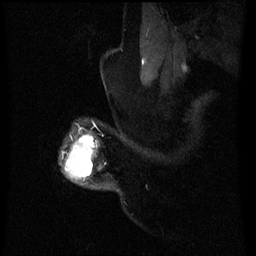
Breast MRI (dynamic contrast-enhanced), one sagittal slice; slice 55 of 60 in the series (ordered by position); dynamic contrast-enhanced series, image 2 of 3 at this slice position (ordered by acquisition); 1.5 T; TE 4.2 ms, TR 8 ms; 2.5 mm slice thickness; 256 × 256 image matrix, field of view 200 × 200 mm. Patient: female, 50 years.
Structures marked on this image (semi-automatic segmentation, software-assisted and operator-edited):
- analysis volume of interest (the breast-tissue region the enhancement analysis was run in; not a lesion): bounding box <66,136,97,179> (left, top, right, bottom; pixels)
- tumour enhancement mask (voxels above the 70 % enhancement threshold inside the analysis volume of interest): <79,138,93,145>